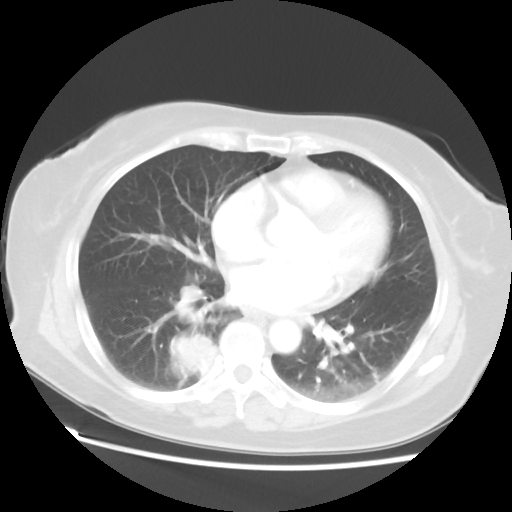
Chest CT, one axial slice. Position 24 of 52 along the scan axis. Reconstruction kernel STANDARD. Lung window (W 1500 / L -600 HU). 5 mm slice thickness. 512 × 512 image matrix, field of view 356 × 356 mm. Female patient, age 69 years. From the clinical record (not read from this slice): clinical TNM (as recorded): T2 N1 M1a.
Annotated regions visible in this slice (rectangle marked by the reading radiologist):
- lung tumour (recorded histology: adenocarcinoma): bounding box (x1, y1, x2, y2) in pixels: (163, 325, 216, 378)